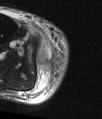
MRI of an extremity soft-tissue mass, one axial slice. Position 11 of 48 along the scan axis. T2-weighted fat-saturated. MR volume resampled by the dataset authors to the PET/CT grid (not the native acquisition matrix). 3.27 mm slice thickness. 102 × 119 image matrix, field of view 100 × 116 mm. Male patient. From the clinical record (not read from this slice): histological type: pleiomorphic liposarcoma; grade: high; site of the primary tumour: right calf.
Outlined on this slice (expert contour drawn on MRI and transferred to this co-registered scan by the dataset authors):
- gross tumour volume including surrounding oedema: bounding box <39,56,49,68> (left, top, right, bottom; pixels)